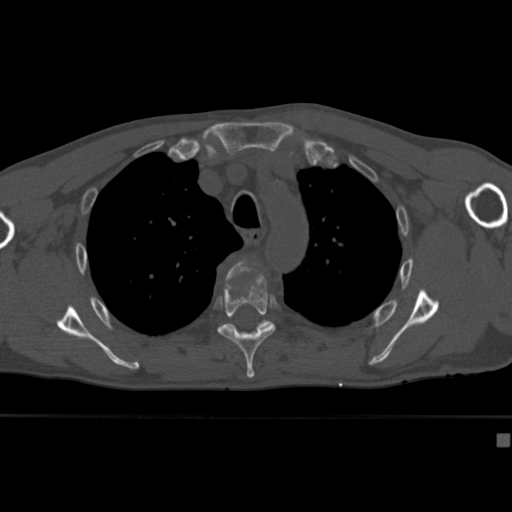
CT including the spine, one axial slice; position 309 of 430 along the scan axis; 120 kVp; bone window (W 1800 / L 400 HU); 512 × 512 image matrix, field of view 337 × 337 mm. Patient: male, 64 years. Case-level facts recorded for this patient, not image findings: primary cancer: uterus; vertebrae with lytic lesions (as recorded): T1, T4, T5, T7, L5.
Annotated regions visible in this slice (semi-automatic segmentation, software-assisted and operator-edited):
- T4 vertebra: box from (x=225, y=257) to (x=261, y=280) px
- T5 vertebra: (x=217, y=273)–(x=276, y=379)
- T6 vertebra: (x=224, y=319)–(x=271, y=331)